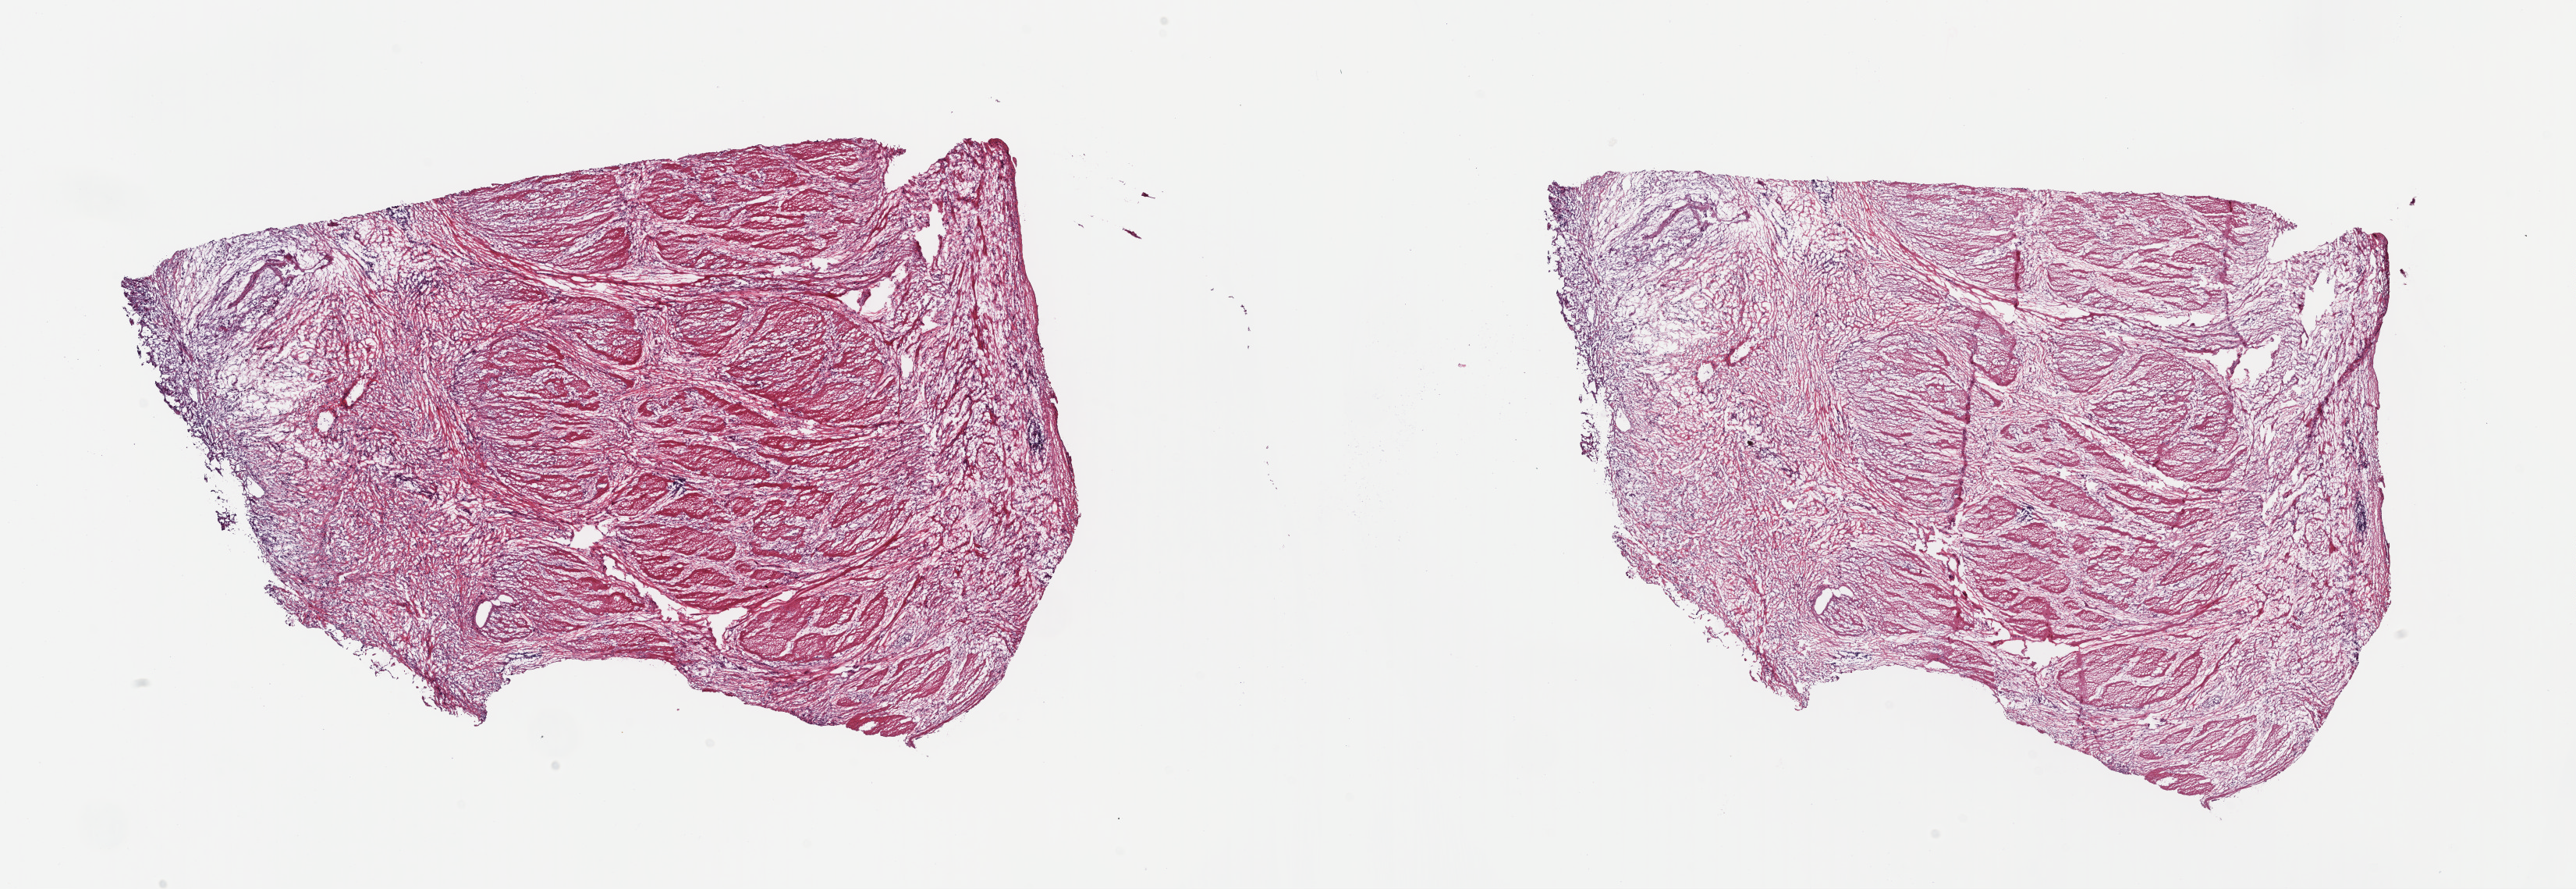
Whole-slide histology image, Hematoxylin and eosin (H&E) stained, low-resolution overview of the scanned area, about 26.0 x 9.0 mm. Frozen section from the top of the tissue portion. Stomach, primary tumour sample. Patient: male, age at initial diagnosis 55 years. Histologic grade: G3 (poorly differentiated). Pathologist review of this section (percent, as recorded): tumour cells 25%, tumour nuclei 75%, normal cells 0%, stromal cells 60%, necrosis 15%. Infiltration values recorded for this section: lymphocyte infiltration 3%, monocyte infiltration 0%, neutrophil infiltration 0%.
* diagnosis: Adenocarcinoma, NOS (gastric antrum)
* lymph nodes positive (case pathology): 0 of 10 examined
* AJCC pathologic stage: IIA (7th edition)
* TNM: T3 N0 M0